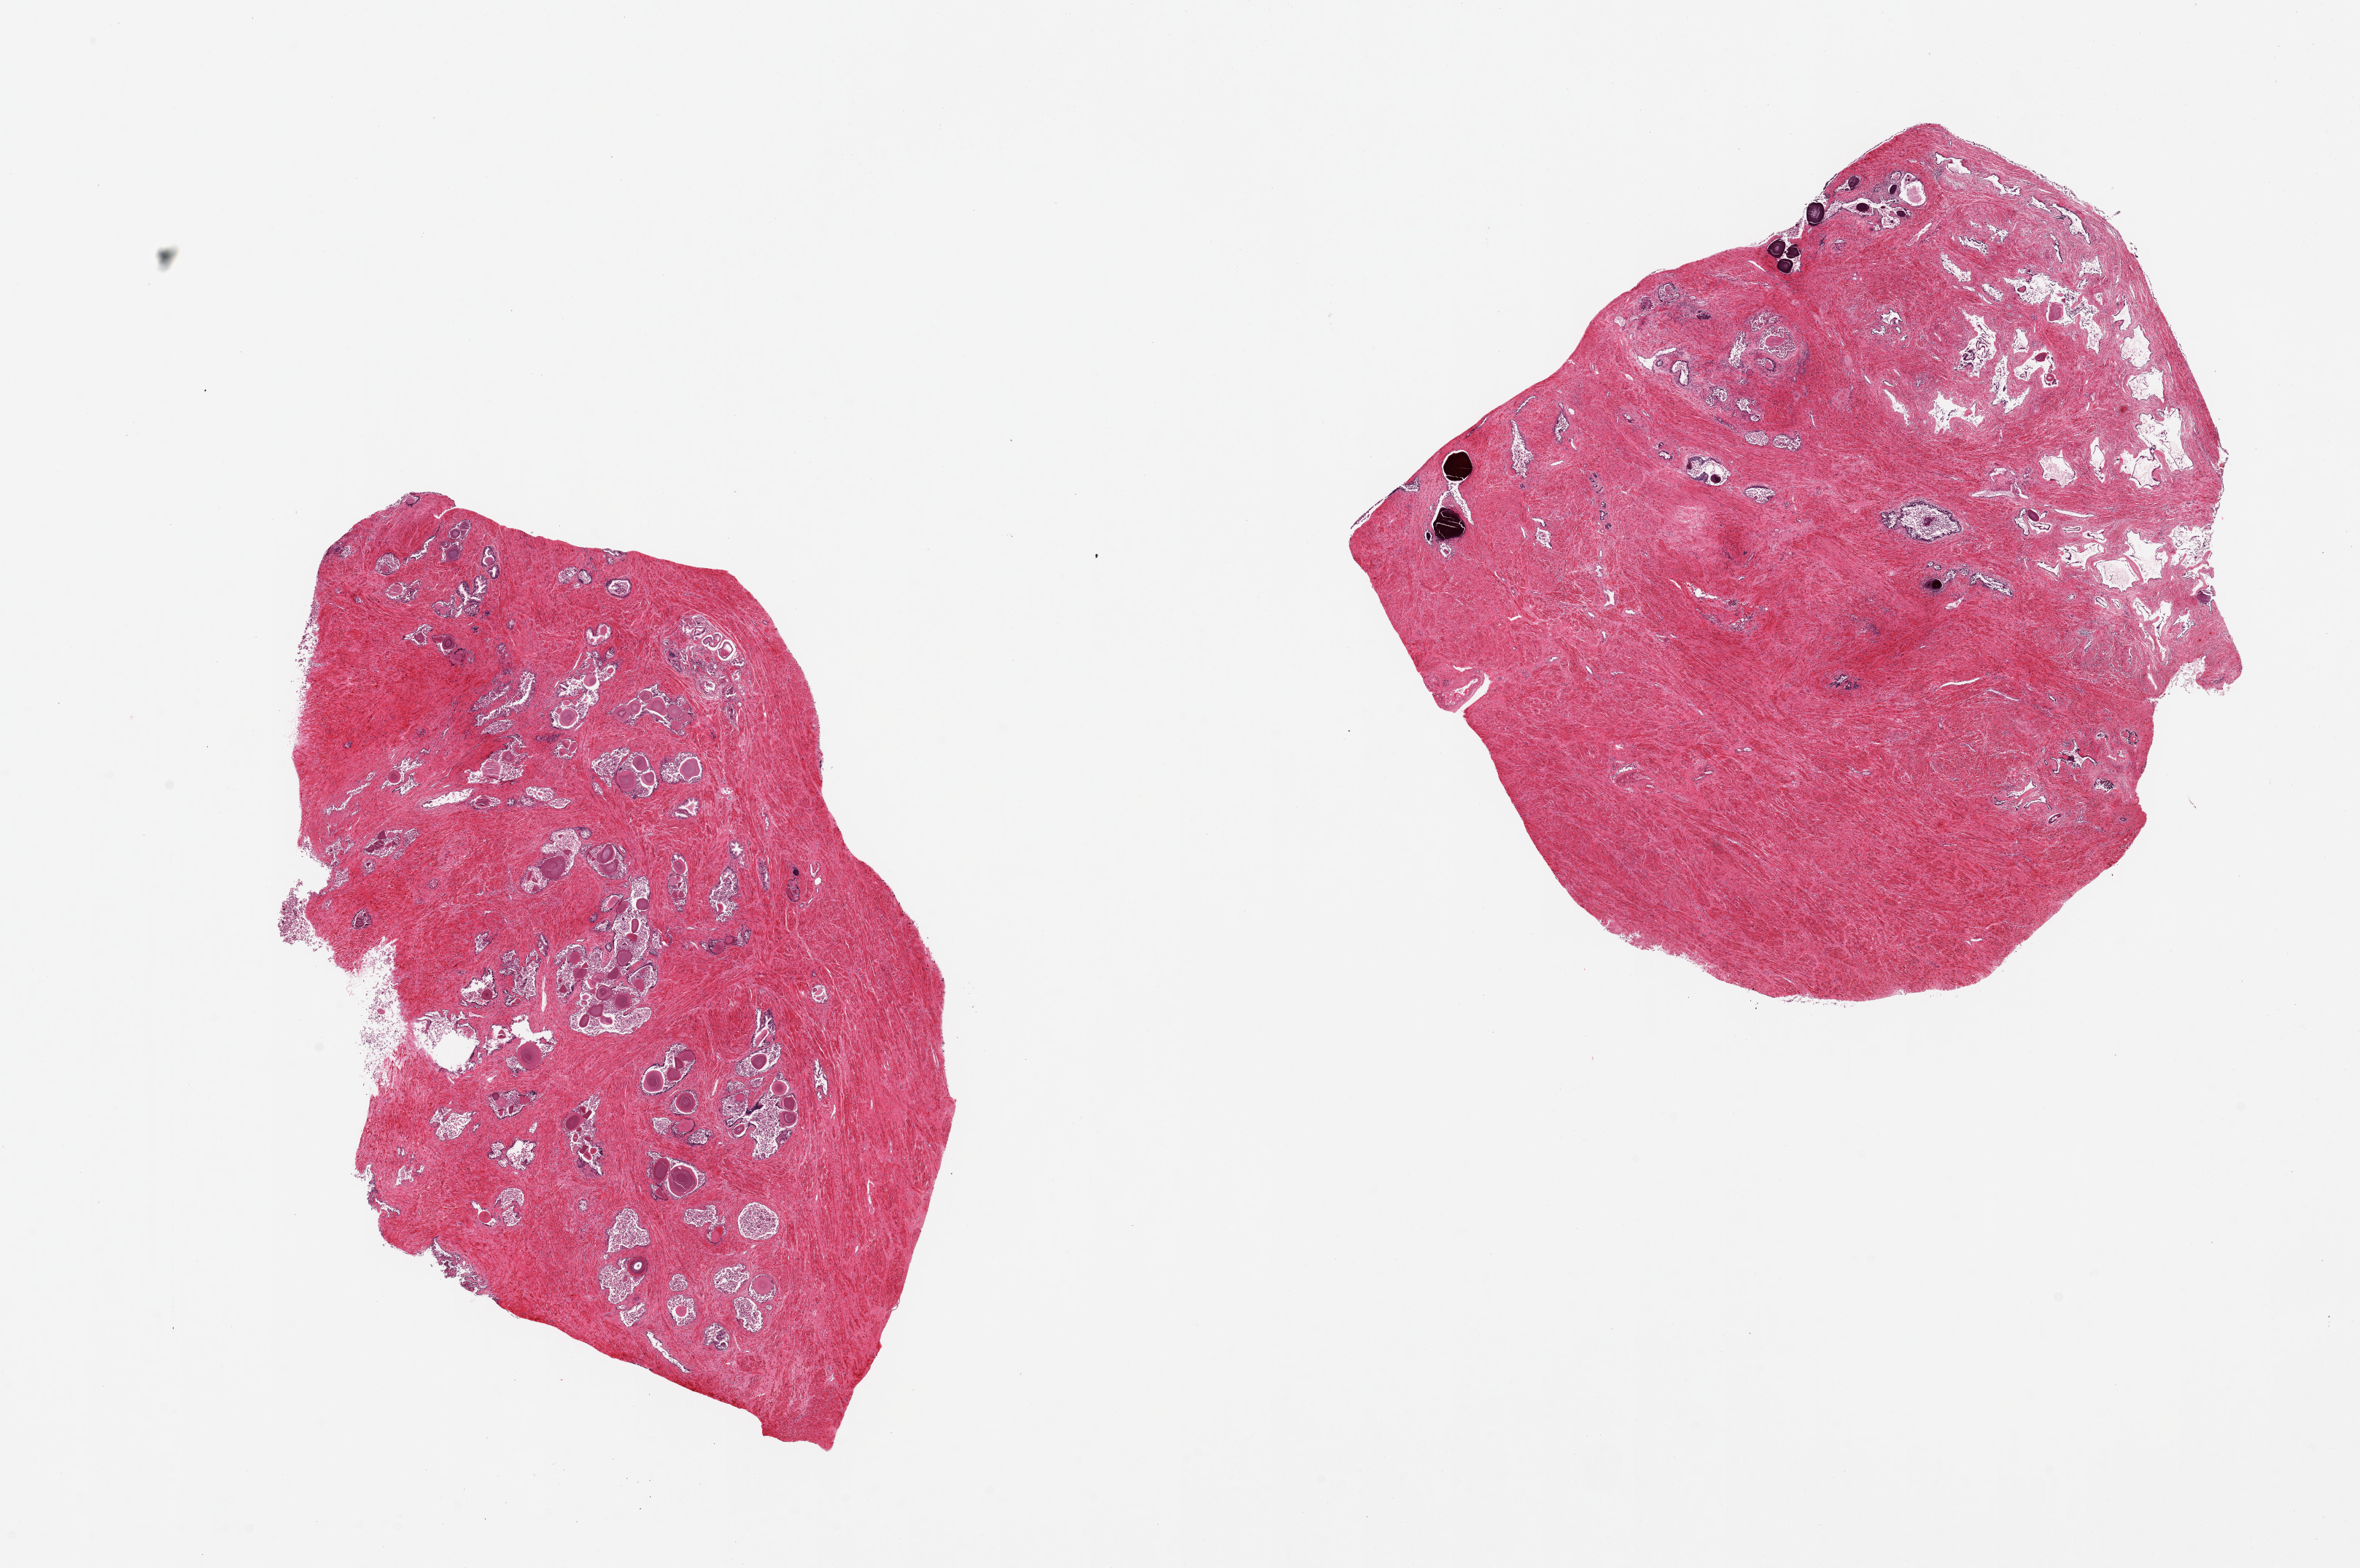
Haematoxylin and eosin whole-slide image, brightfield, shown as a low-resolution overview of the whole scanned area (about 25.6 x 17.0 mm). PAXgene-fixed, paraffin-embedded tissue. Sampled site (target tissue): prostate. Tissue donor sample. Male donor.
- reviewer comment on this tissue sample: 2 pieces; autolyzed glands, preserved muscular stroma